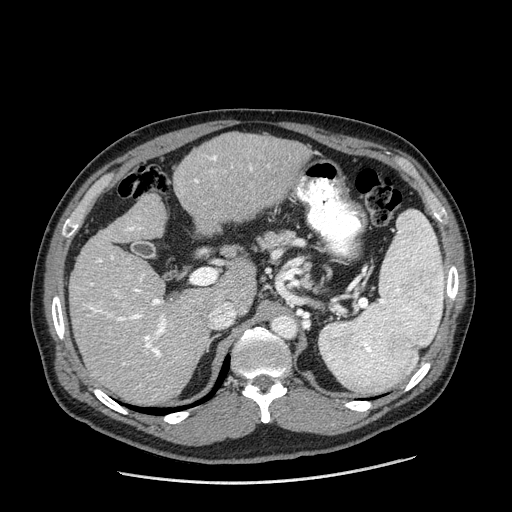
Contrast-enhanced abdominal CT (liver protocol), one axial slice; slice 111 of 198 in the series (ordered by position); reconstruction kernel STANDARD; 120 kVp; one of 2 acquisitions stored at this slice position; soft-tissue window (W 400 / L 40 HU); 2.5 mm slice thickness; 512 × 512 image matrix. From the clinical record (not read from this slice): diagnosis: hepatocellular carcinoma (patient treated with transarterial chemoembolisation; whether this scan precedes or follows treatment is not stated here); TNM stage (as recorded): Stage-II; Child-Pugh class: A; tumour nodularity: multinodular; tumour size: 2.6 cm.
Structures marked on this image (semi-automatic segmentation, software-assisted and operator-edited):
- liver parenchyma outside the tumour (the mass and vessels are separate outlines, so this box may not span the whole liver): bounding box <68,132,310,404> (left, top, right, bottom; pixels)
- liver vessels: <88,155,253,365>